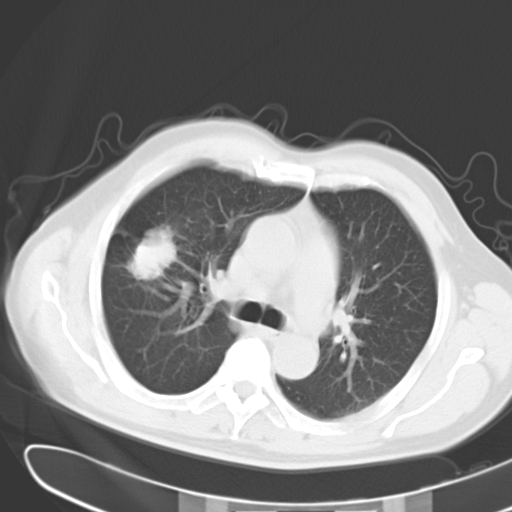
Chest CT, one axial slice; position 20 of 31 along the scan axis; reconstruction kernel B40f; lung window (W 1500 / L -600 HU); 10 mm slice thickness; 512 × 512 image matrix, field of view 364 × 364 mm. Male patient, age 59 years. From the clinical record (not read from this slice): clinical TNM (as recorded): T2 N3 M0.
Structures marked on this image (rectangle marked by the reading radiologist):
- lung tumour (recorded histology: adenocarcinoma): box from (x=128, y=236) to (x=180, y=281) px